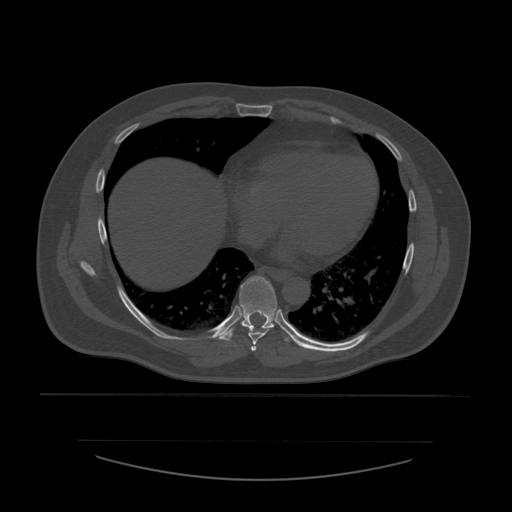
CT including the spine, one axial slice. Position 347 of 532 along the scan axis. Reconstruction kernel STANDARD. Bone window (W 1800 / L 400 HU). 1.25 mm slice thickness. 512 × 512 image matrix, field of view 441 × 441 mm. Patient age 44 years. From the clinical record (not read from this slice): primary cancer: soft tissue sarcoma.
Structures marked on this image (semi-automatic segmentation, software-assisted and operator-edited):
- T6 vertebra: bounding box (x1, y1, x2, y2) in pixels: (251, 346, 257, 353)
- T7 vertebra: (248, 329, 270, 345)
- T8 vertebra: (217, 276, 293, 342)